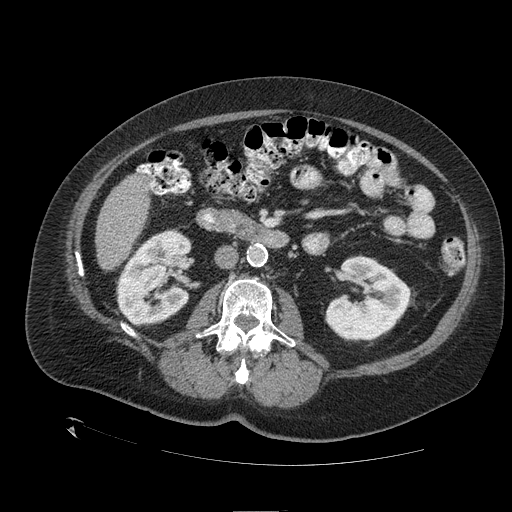
Contrast-enhanced abdominal CT (liver protocol), one axial slice. Slice 39 of 109 in the series (ordered by position). Reconstruction kernel STANDARD. 120 kVp. One of 2 acquisitions stored at this slice position. Soft-tissue window (W 400 / L 40 HU). 2.5 mm slice thickness. 512 × 512 image matrix, field of view 460 × 460 mm. From the clinical record (not read from this slice): diagnosis: hepatocellular carcinoma (patient treated with transarterial chemoembolisation; whether this scan precedes or follows treatment is not stated here); TNM stage (as recorded): Stage-I; Child-Pugh class: A.
Structures marked on this image (semi-automatic segmentation, software-assisted and operator-edited):
- liver parenchyma outside the tumour (the mass and vessels are separate outlines, so this box may not span the whole liver): box from (x=96, y=168) to (x=150, y=270) px